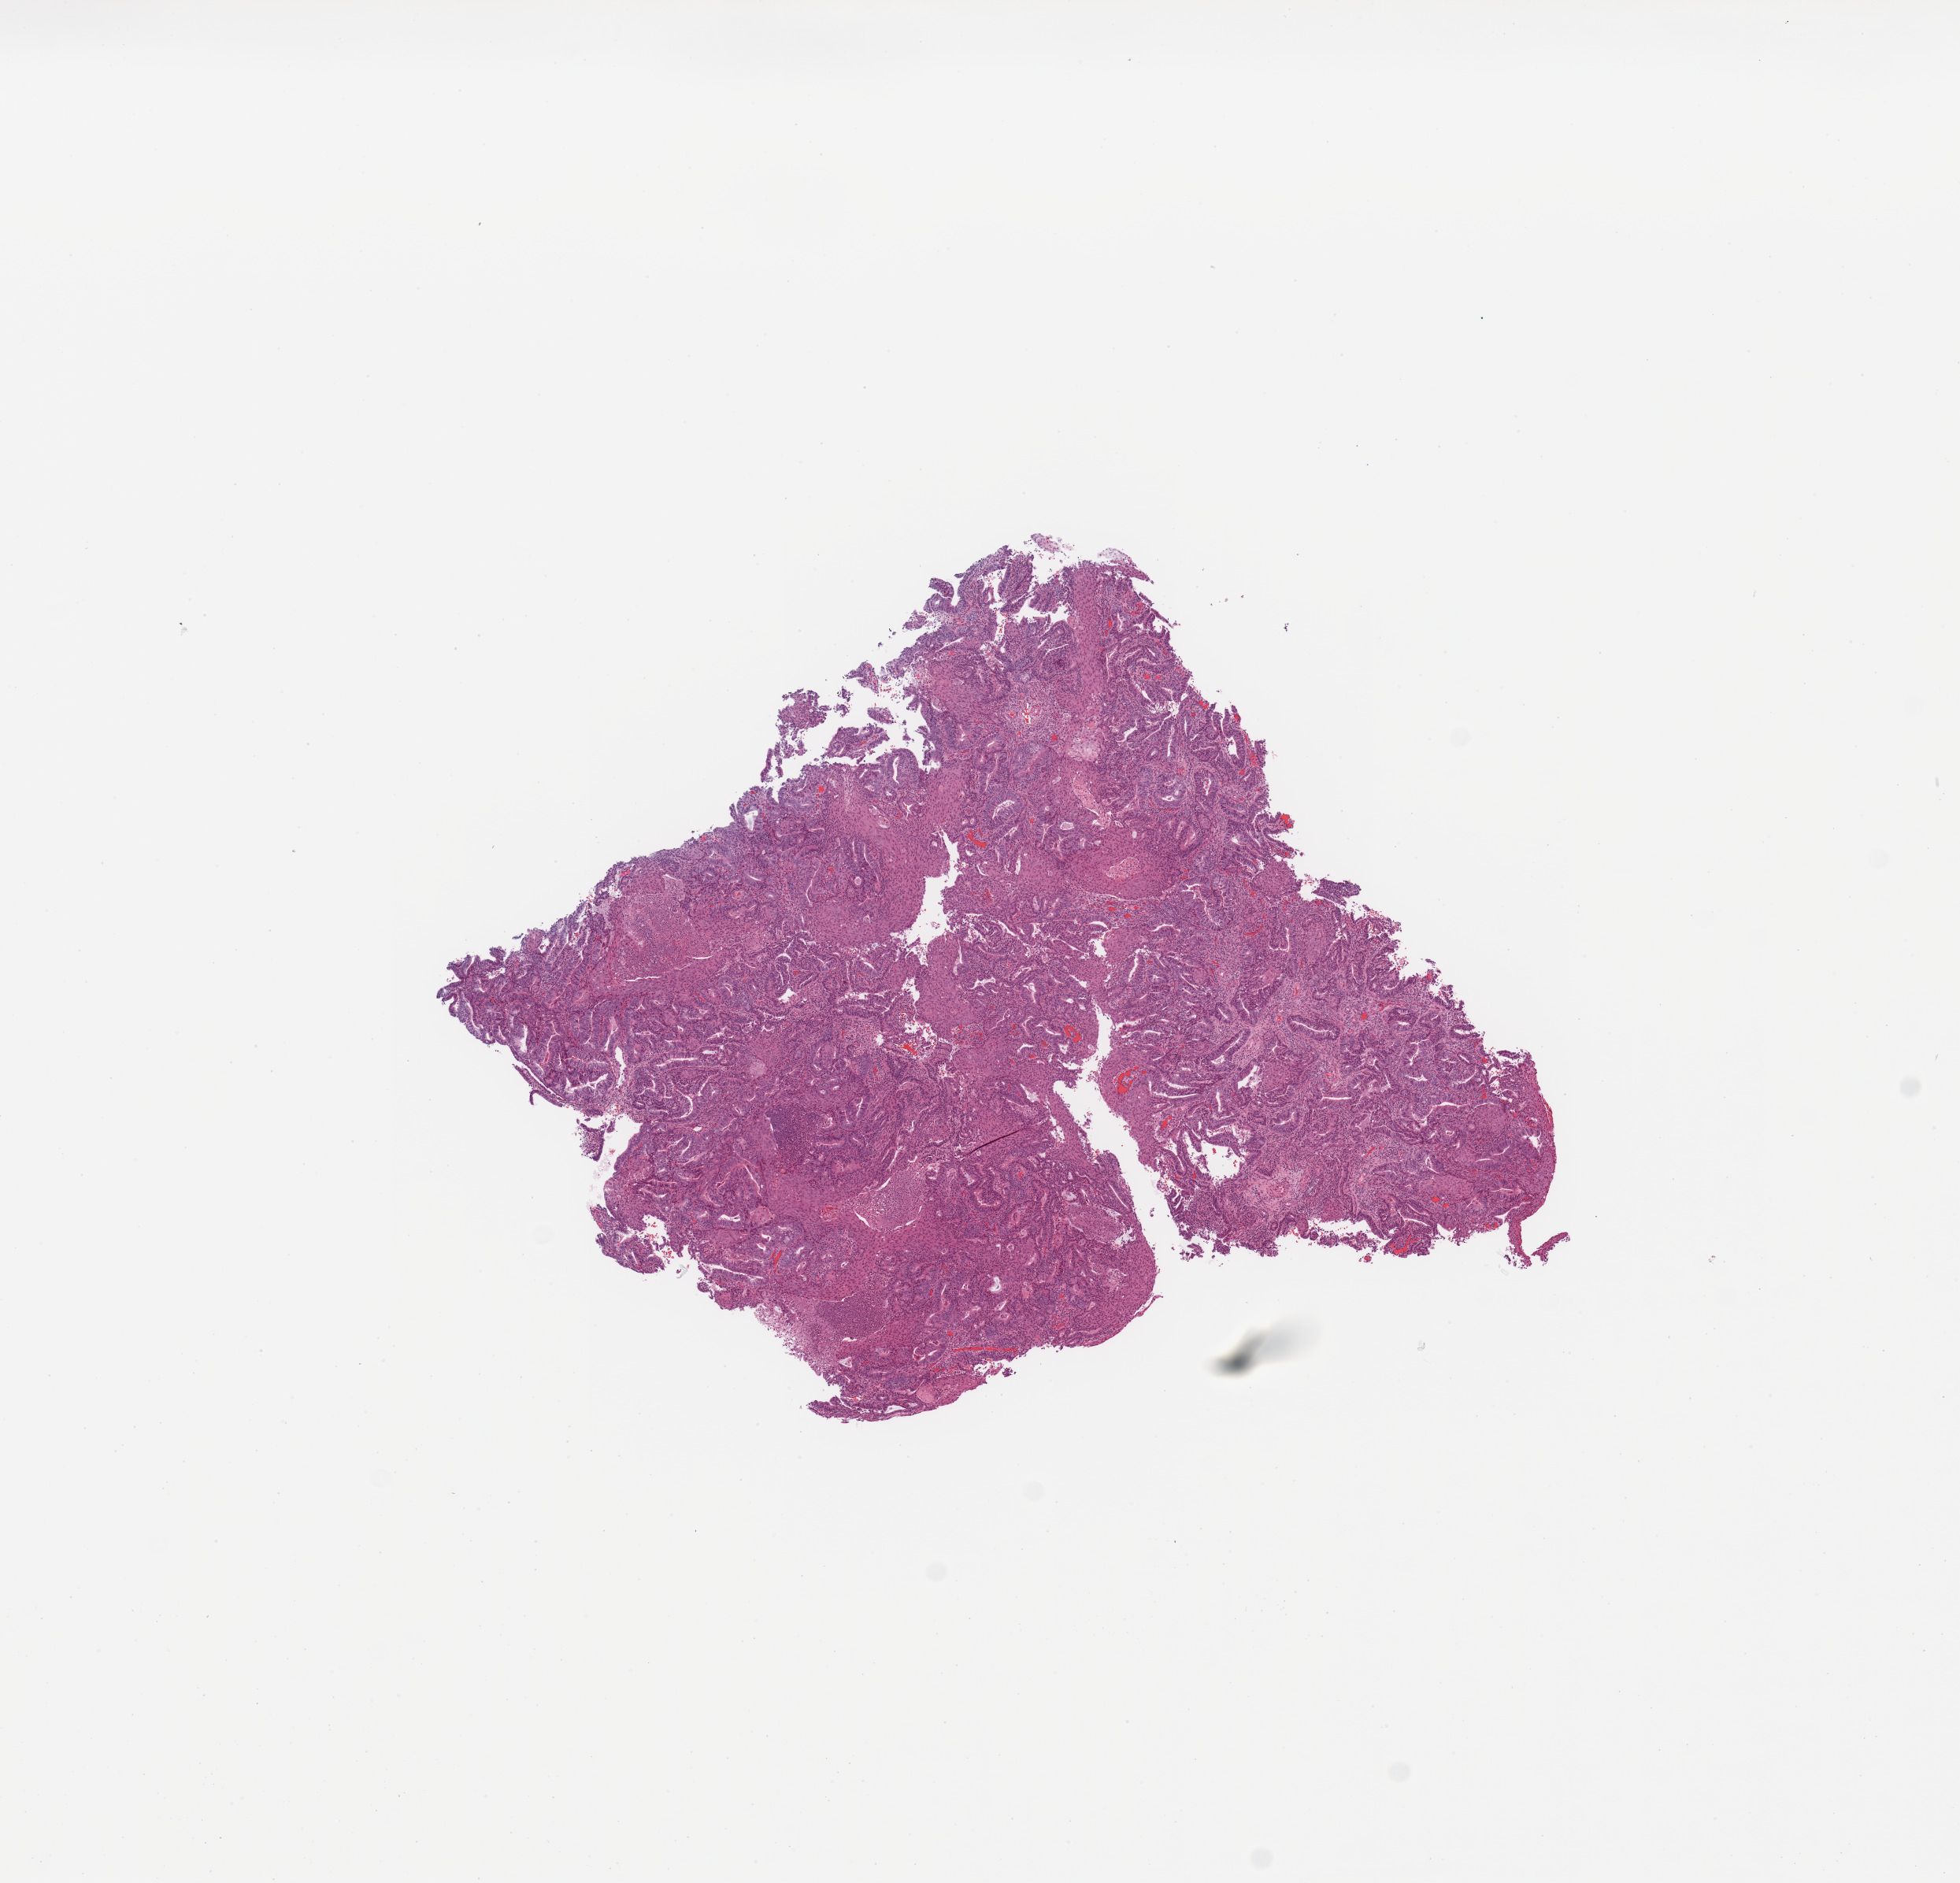
Whole-slide histology image, Hematoxylin and eosin (H&E) stained, shown as a low-resolution overview of the whole scanned area (about 9.8 x 9.5 mm, from a 20x scan); tumour tissue sample, uterus. Female, 56 y/o. Histologic grade: G1 (well differentiated).
* histologic diagnosis: Endometrioid adenocarcinoma, NOS
* AJCC pathologic stage: I